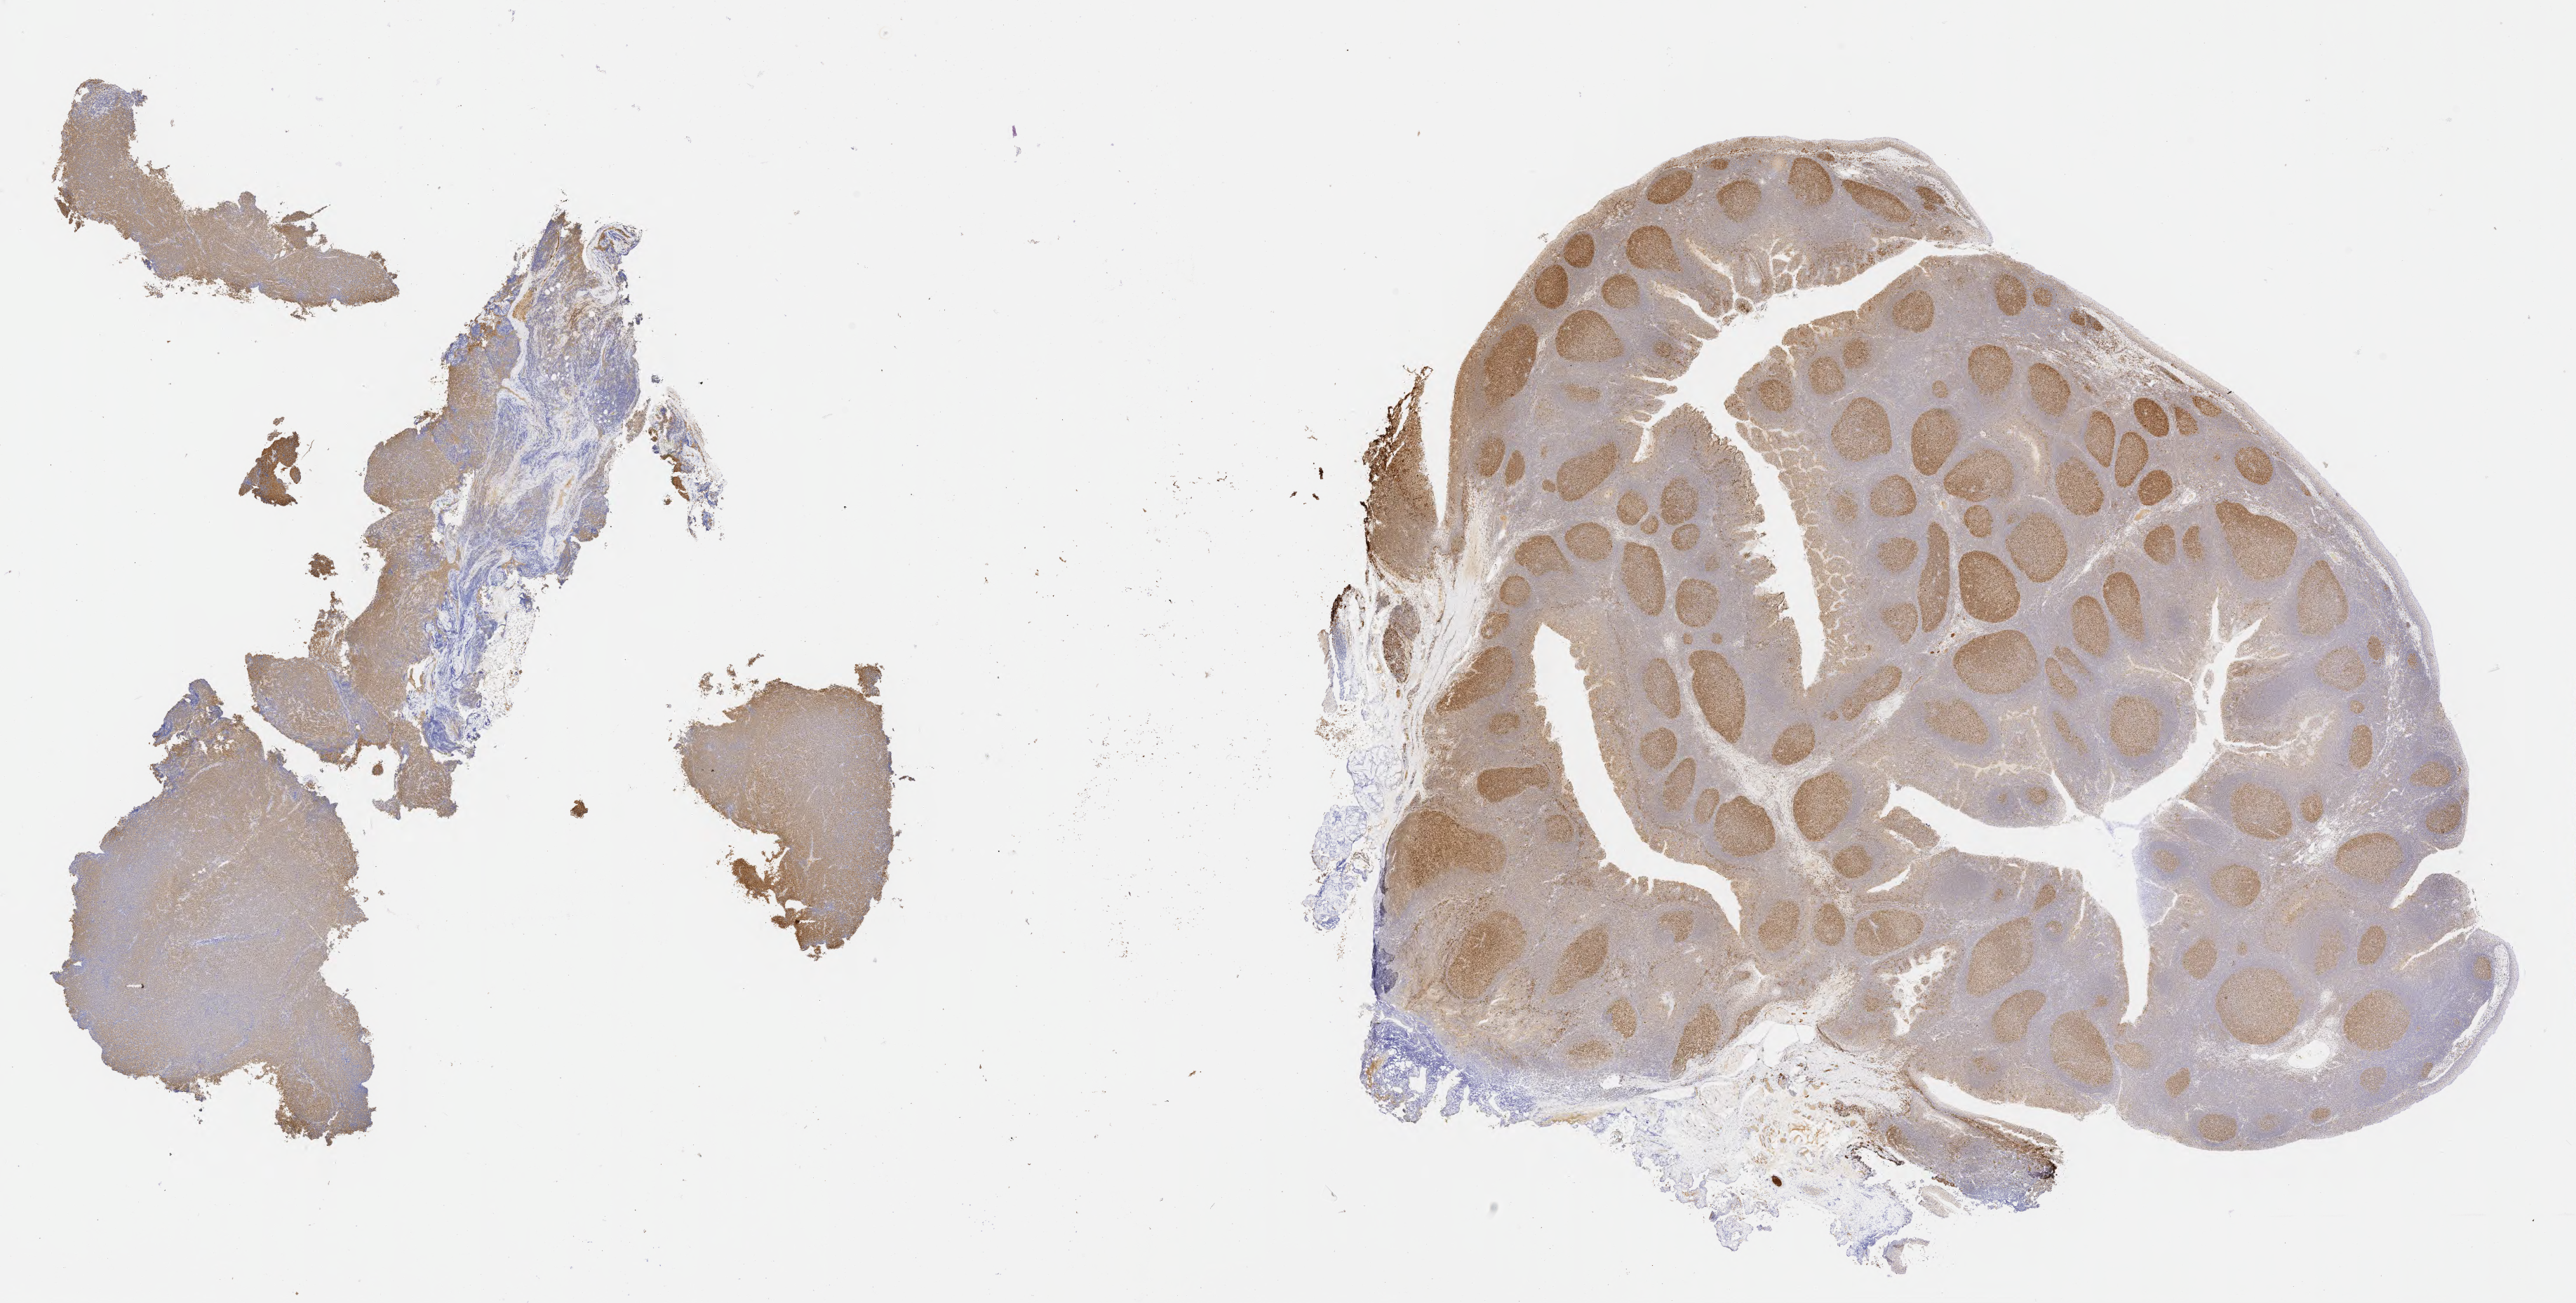
IHC for BCL6, whole-slide image — whole scanned area (about 29.7 x 15.0 mm) shown as a low-resolution overview; tumor tissue; site: liver. Female patient, aged 36.
Diagnosis: Diffuse large B-cell lymphoma, NOS.